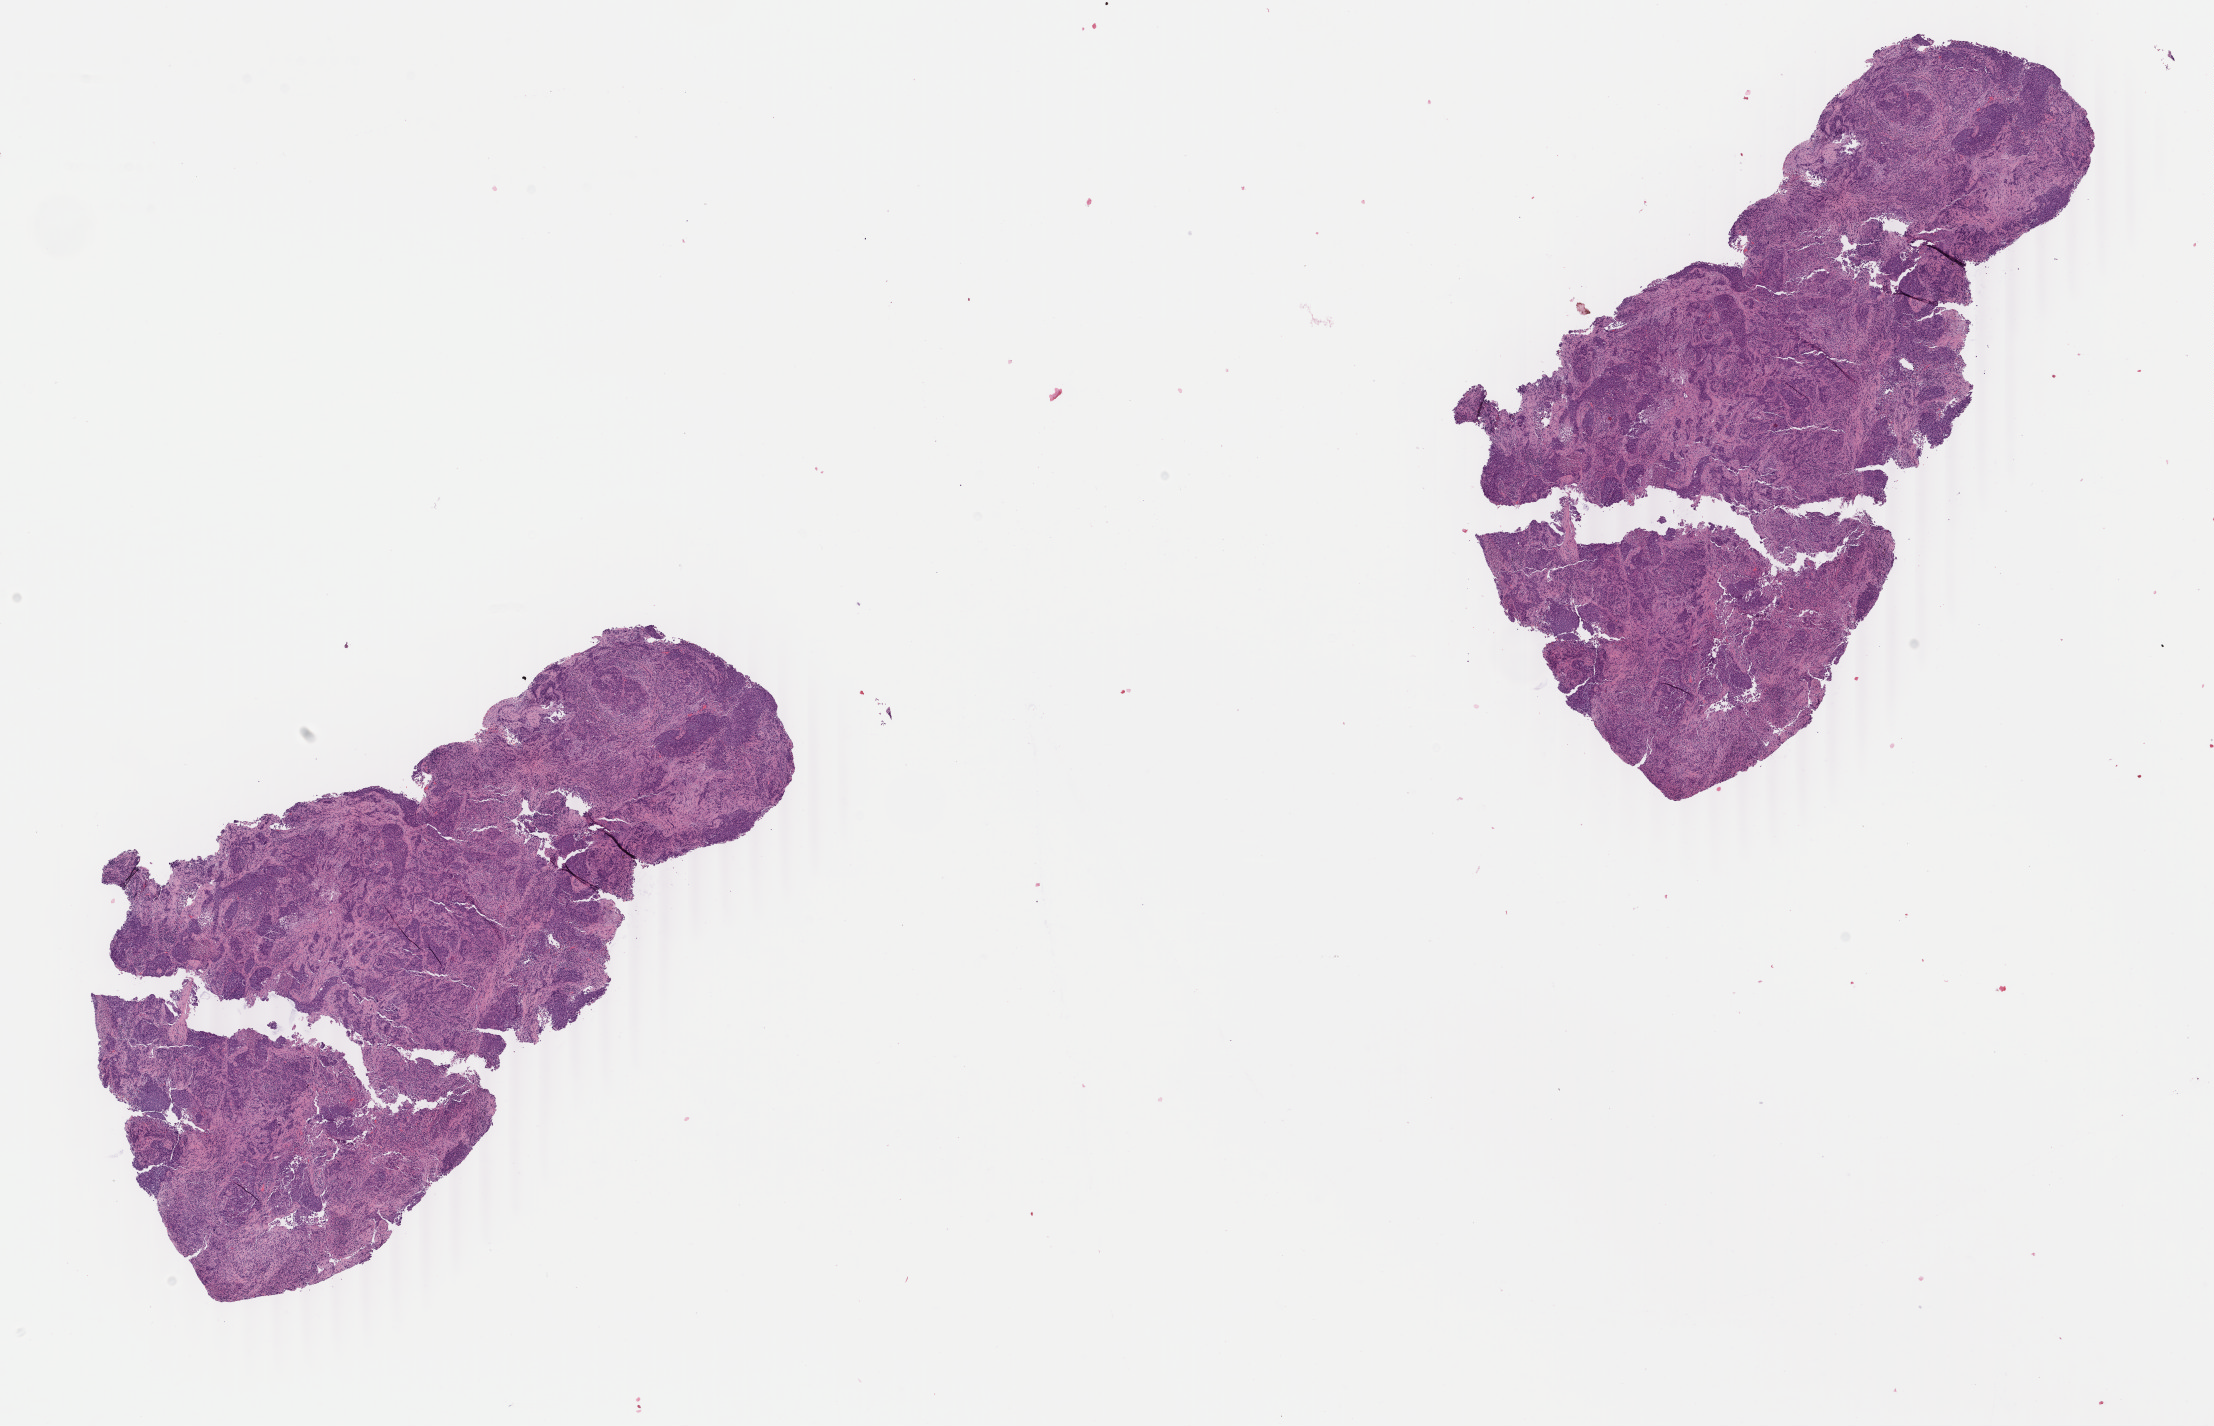
Whole-slide histology image, H&E-stained, a low-resolution overview of the entire scanned area, about 17.6 x 11.3 mm (slide scanned at 40x); formalin-fixed paraffin-embedded (FFPE) diagnostic section; lung, primary tumour sample. Male, age 53 years at initial diagnosis.
AJCC pathologic stage: IIA (7th edition). Histologic diagnosis: Squamous cell carcinoma, NOS. TNM: T2a N1 MX.